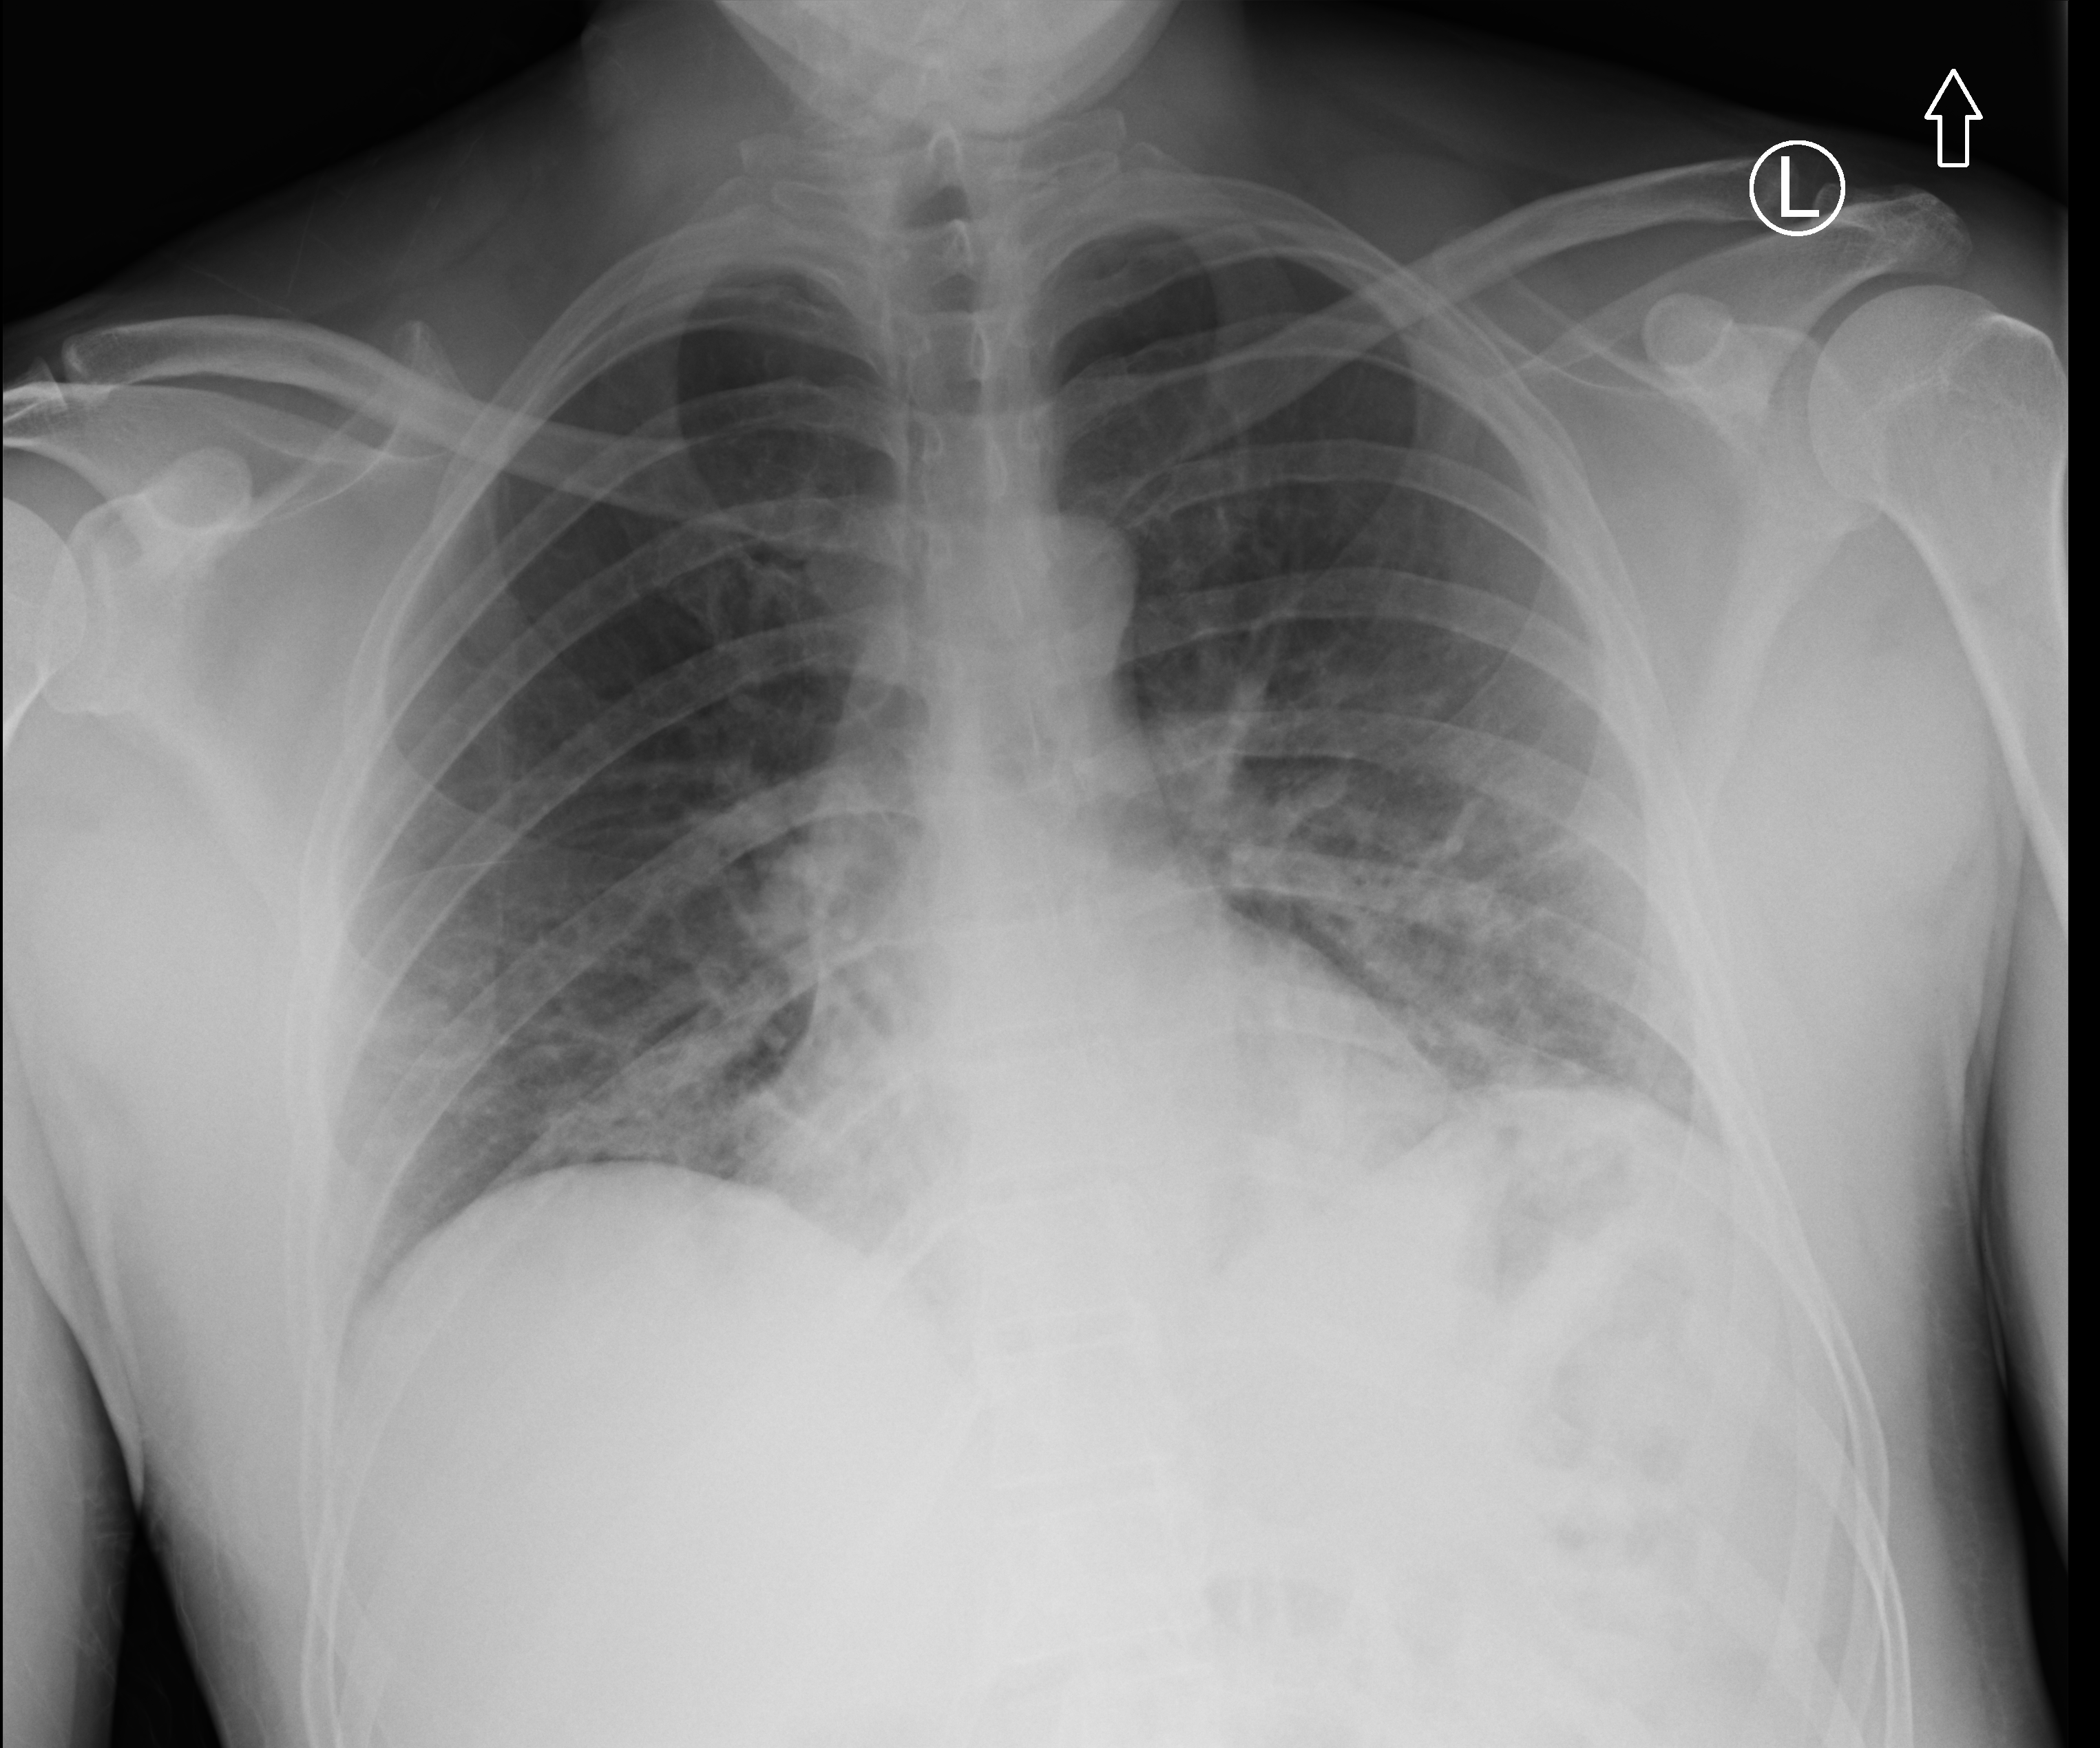
Bedside chest radiograph (computed radiography); anteroposterior (AP) projection. Male patient hospitalised with COVID-19, age 18–59 years.
Hospital-stay facts (about this admission, not read from this image; timing relative to this image not recorded): hypertension (admission record): no; admitted to intensive care during this hospital stay: no; mechanically ventilated during this hospital stay: no.